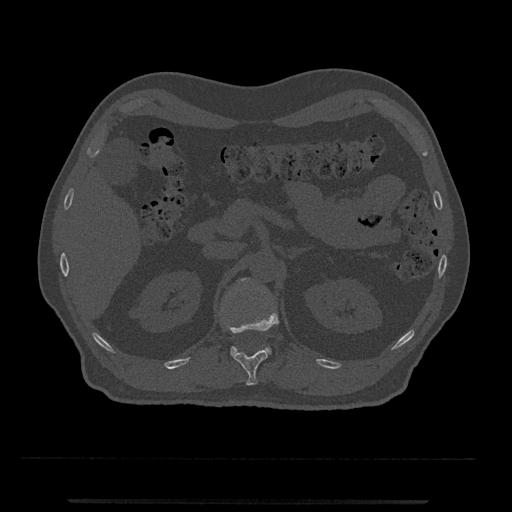
CT including the spine, one axial slice. Slice 376 of 797 in the series (ordered by position). Reconstruction kernel Br40s/3. Bone window (W 1800 / L 400 HU). 0.5 mm slice thickness. 512 × 512 image matrix, field of view 419 × 419 mm. Patient: male, 63 years. From the clinical record (not read from this slice): primary cancer: prostate.
Structures marked on this image (semi-automatically segmented with operator editing):
- L1 vertebra: bounding box <230,278,272,356> (left, top, right, bottom; pixels)
- T12 vertebra: <224,307,279,386>